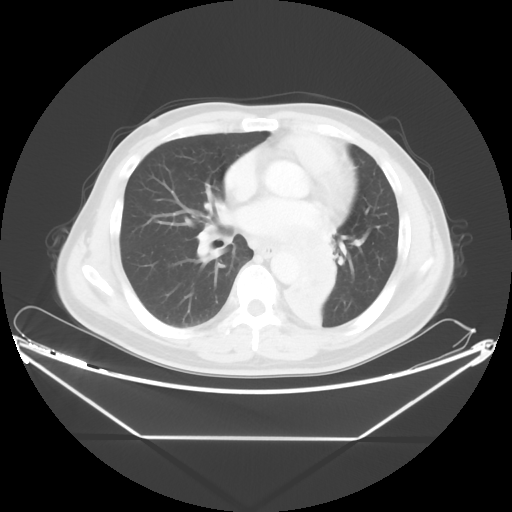
Chest CT, one axial slice; slice 22 of 48 in the series (ordered by position); reconstruction kernel STANDARD; lung window (W 1500 / L -600 HU); 512 × 512 image matrix. Male patient, age 58 years. Case-level facts recorded for this patient, not image findings: clinical TNM (as recorded): T3 N3 M0.
Annotated regions visible in this slice (bounding box drawn by a radiologist):
- lung tumour (recorded histology: squamous cell carcinoma): box from (x=281, y=217) to (x=357, y=339) px